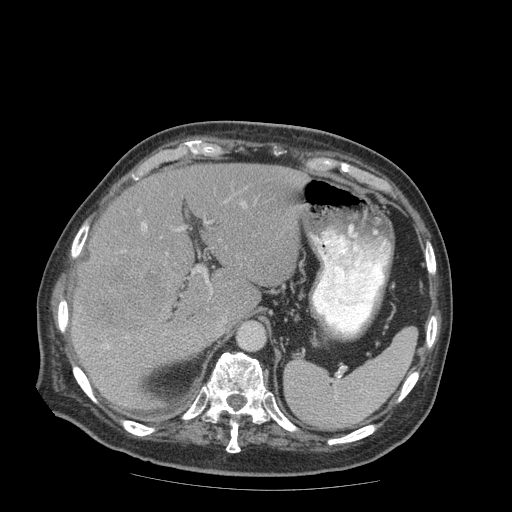
Contrast-enhanced abdominal CT (liver protocol), one axial slice. Slice 58 of 99 in the series (ordered by position). Soft-tissue window (W 400 / L 40 HU). 2.5 mm slice thickness. 512 × 512 image matrix, field of view 420 × 420 mm. From the clinical record (not read from this slice): diagnosis: hepatocellular carcinoma (patient treated with transarterial chemoembolisation; whether this scan precedes or follows treatment is not stated here); TNM stage (as recorded): Stage-IIIB; Child-Pugh class: A; tumour differentiation: well differentiated; tumour nodularity: multinodular.
Annotated regions visible in this slice (semi-automatically segmented with operator editing):
- liver parenchyma outside the tumour (the mass and vessels are separate outlines, so this box may not span the whole liver): bounding box (x1, y1, x2, y2) in pixels: (70, 164, 306, 408)
- mass: (73, 242, 180, 342)
- liver vessels: (105, 202, 245, 349)